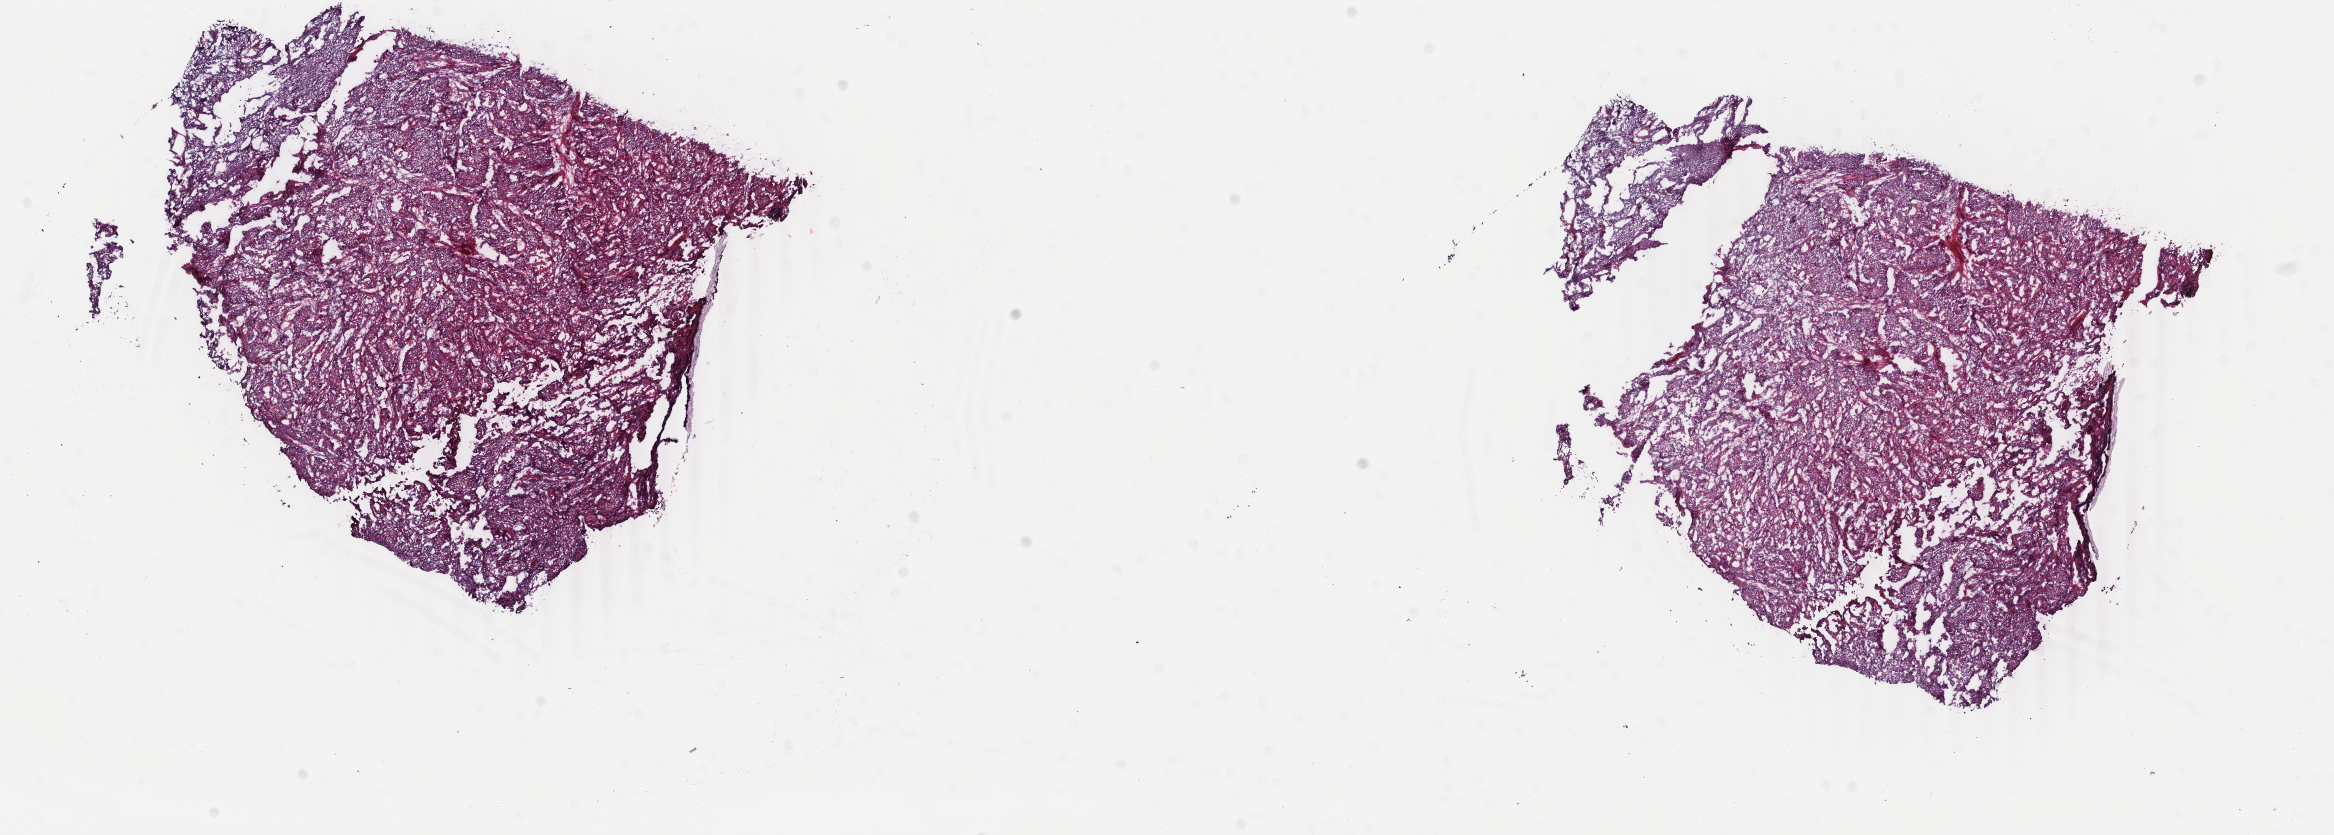
Digitized Hematoxylin and eosin (H&E) stained tissue section (whole slide) — whole scanned area (about 18.6 x 6.6 mm) shown as a low-resolution overview; frozen section; sample: primary tumour, cervix. Female patient; age at initial diagnosis 80 years. Pathologist review of this section (percent, as recorded): tumour cells 100%, tumour nuclei 75%.
Histologic diagnosis: Squamous cell carcinoma, NOS (cervix uteri).